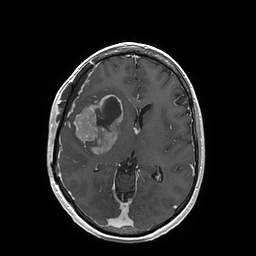
Brain MRI from a brain-tumour surgery series, one axial slice. Slice 87 of 202 in the series (ordered by position). T1-weighted post-contrast. 1 mm slice thickness. 256 × 256 image matrix, field of view 250 × 250 mm. Case-level facts recorded for this patient, not image findings: histopathology: Glioblastoma; WHO grade: 4; IDH mutation: no.
Annotated regions visible in this slice (outlined manually by an expert reader):
- tumour: box from (x=74, y=95) to (x=123, y=154) px